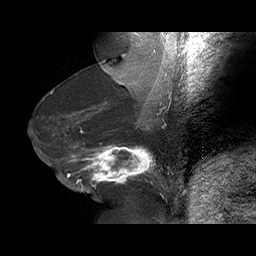
Breast MRI (dynamic contrast-enhanced), one sagittal slice. Slice 34 of 75 in the series (ordered by position). Dynamic contrast-enhanced series, time point 2 of 6 at this slice position (early post-contrast). 1.5 T. TE 4.5 ms, TR 32.4 ms. 256 × 256 image matrix, field of view 180 × 180 mm. Female patient. From the clinical record (not read from this slice): setting: breast cancer imaged before/during neoadjuvant chemotherapy; receptor status: HR-positive, HER2-negative.
Structures marked on this image (semi-automatic segmentation, software-assisted and operator-edited):
- analysis volume of interest (the breast-tissue region the enhancement analysis was run in; not a lesion): bounding box <58,134,166,191> (left, top, right, bottom; pixels)
- tumour enhancement mask (voxels above the 100 % enhancement threshold inside the analysis volume of interest): <67,145,157,186>